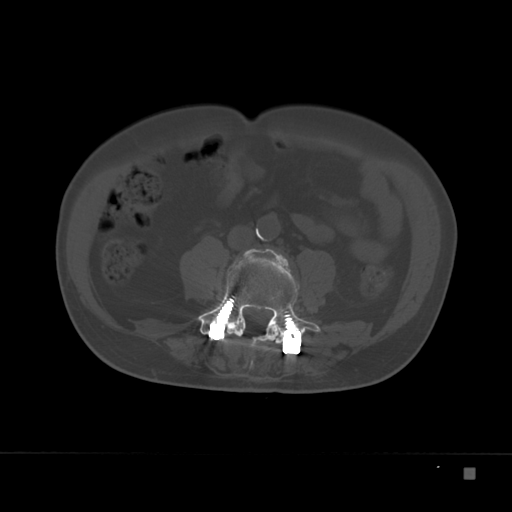
CT including the spine, one axial slice. Slice 50 of 332 in the series (ordered by position). Reconstruction kernel Br40s. Bone window (W 1800 / L 400 HU). 1.5 mm slice thickness. 512 × 512 image matrix, field of view 389 × 389 mm. Patient: male, 72 years. Case-level facts recorded for this patient, not image findings: primary cancer: skeletal.
Annotated regions visible in this slice (semi-automatically segmented with operator editing):
- L3 vertebra: bounding box <265,250,290,267> (left, top, right, bottom; pixels)
- L4 vertebra: <198,249,322,345>